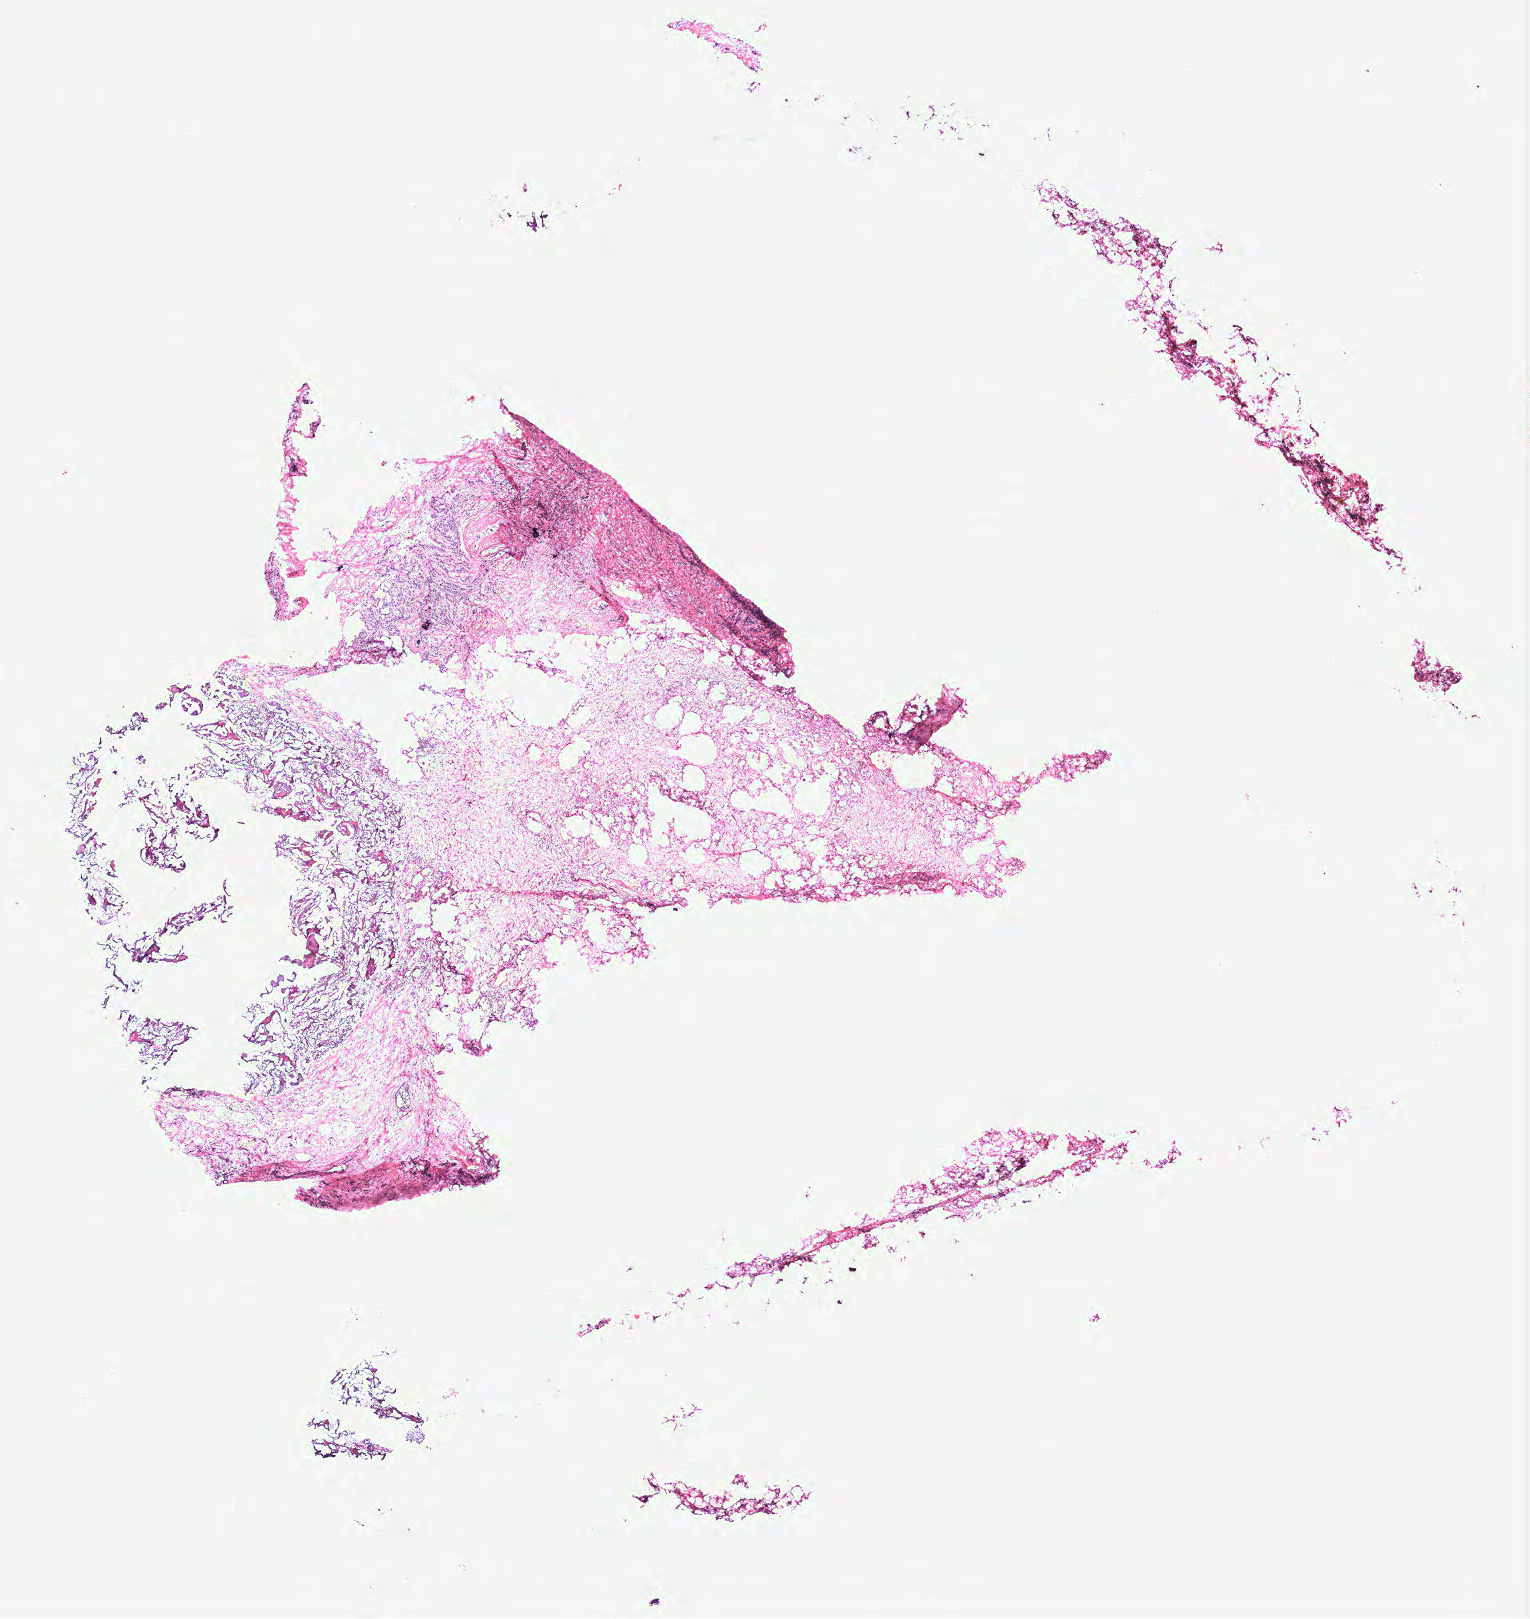
Digitized Hematoxylin and eosin (H&E) stained tissue section (whole slide) — whole scanned area (about 12.2 x 13.0 mm, from a 40x scan) shown as a low-resolution overview, breast, tissue type not recorded.
Patient diagnosis (cohort enrolment): breast cancer (breast).